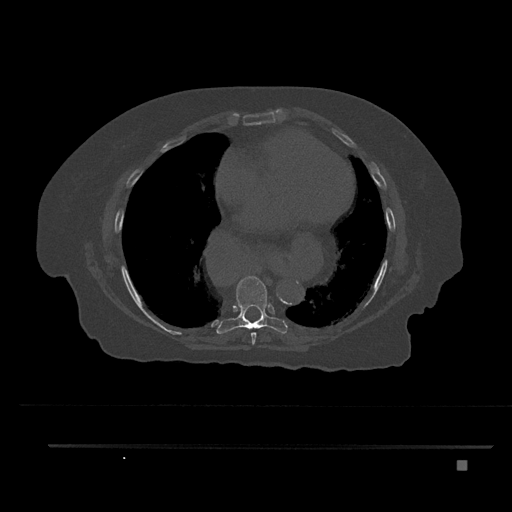
CT including the spine, one axial slice; slice 450 of 797 in the series (ordered by position); reconstruction kernel Br40s/3; 120 kVp; bone window (W 1800 / L 400 HU); 0.5 mm slice thickness; 512 × 512 image matrix, field of view 437 × 437 mm. Female patient, age 76 years. From the clinical record (not read from this slice): primary cancer: lung; vertebrae with lytic lesions (as recorded): T11, L3.
Annotated regions visible in this slice (semi-automatic segmentation, software-assisted and operator-edited):
- T7 vertebra: bounding box [x1, y1, x2, y2] px = [251, 332, 257, 345]
- T8 vertebra: [216, 276, 288, 334]